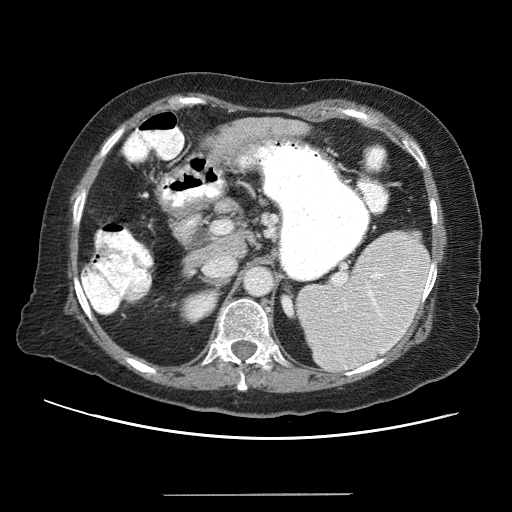
Contrast-enhanced abdominal CT (liver protocol), one axial slice. Slice 30 of 65 in the series (ordered by position). Reconstruction kernel STANDARD. Soft-tissue window (W 400 / L 40 HU). 2.5 mm slice thickness. 512 × 512 image matrix, field of view 380 × 380 mm. From the clinical record (not read from this slice): diagnosis: hepatocellular carcinoma (patient treated with transarterial chemoembolisation; whether this scan precedes or follows treatment is not stated here); TNM stage (as recorded): Stage-IIIB; Child-Pugh class: A; tumour differentiation: moderately differentiated; tumour nodularity: uninodular.
Annotated regions visible in this slice (semi-automatic segmentation, software-assisted and operator-edited):
- liver parenchyma outside the tumour (the mass and vessels are separate outlines, so this box may not span the whole liver): bounding box (x1, y1, x2, y2) in pixels: (183, 116, 310, 273)
- liver vessels: (202, 157, 236, 257)